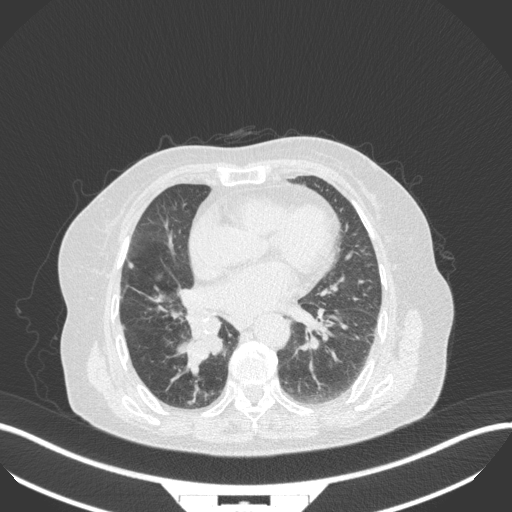
Chest CT, one axial slice; position 140 of 329 along the scan axis; lung window (W 1500 / L -600 HU); 1 mm slice thickness; 512 × 512 image matrix, field of view 400 × 400 mm. Female patient, age 75 years. From the clinical record (not read from this slice): clinical TNM (as recorded): T1b N0 M1a.
Outlined on this slice (rectangle marked by the reading radiologist):
- lung tumour (recorded histology: squamous cell carcinoma): box from (x=172, y=311) to (x=221, y=368) px